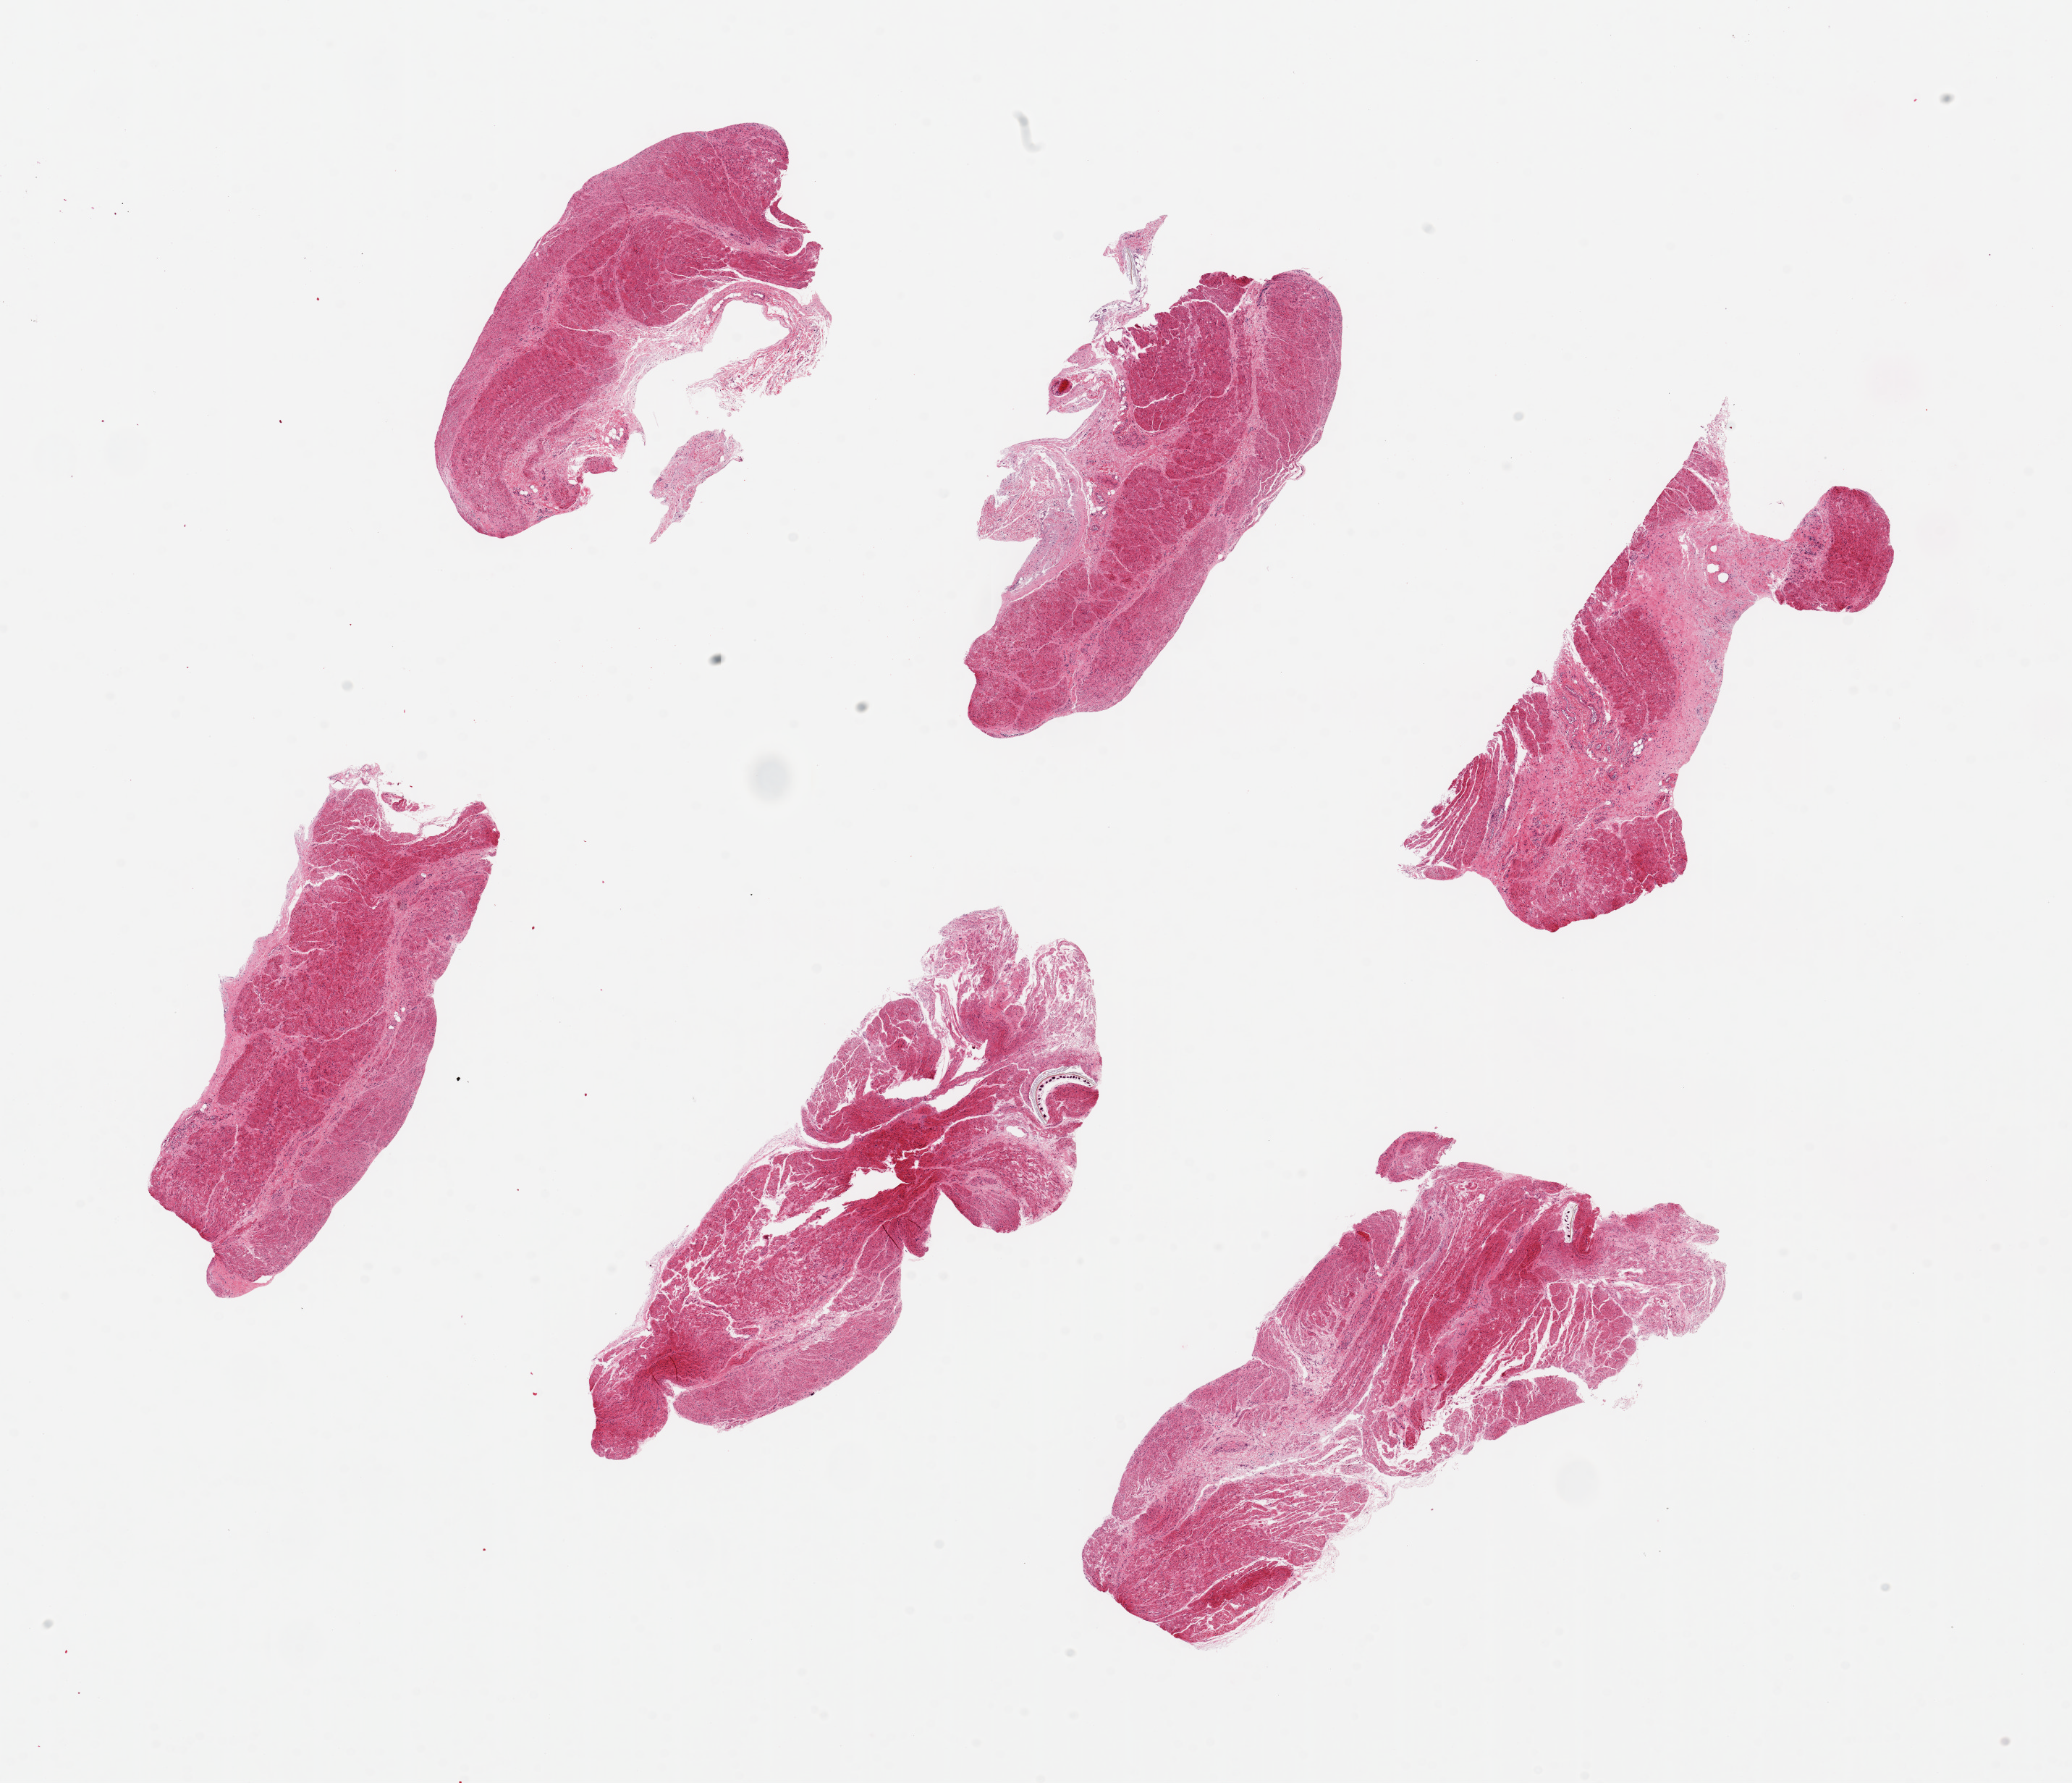
Digitized haematoxylin and eosin-stained section — whole scanned area (about 22.6 x 19.5 mm) shown as a low-resolution overview. PAXgene-fixed paraffin-embedded (PFPE) section. Section of gastroesophageal junction (target tissue). Donor tissue sample. Female donor.
Reviewer comment on this tissue sample: 6 pieces ~6x2mm; Fibrous areas present, ~30% total tissue.